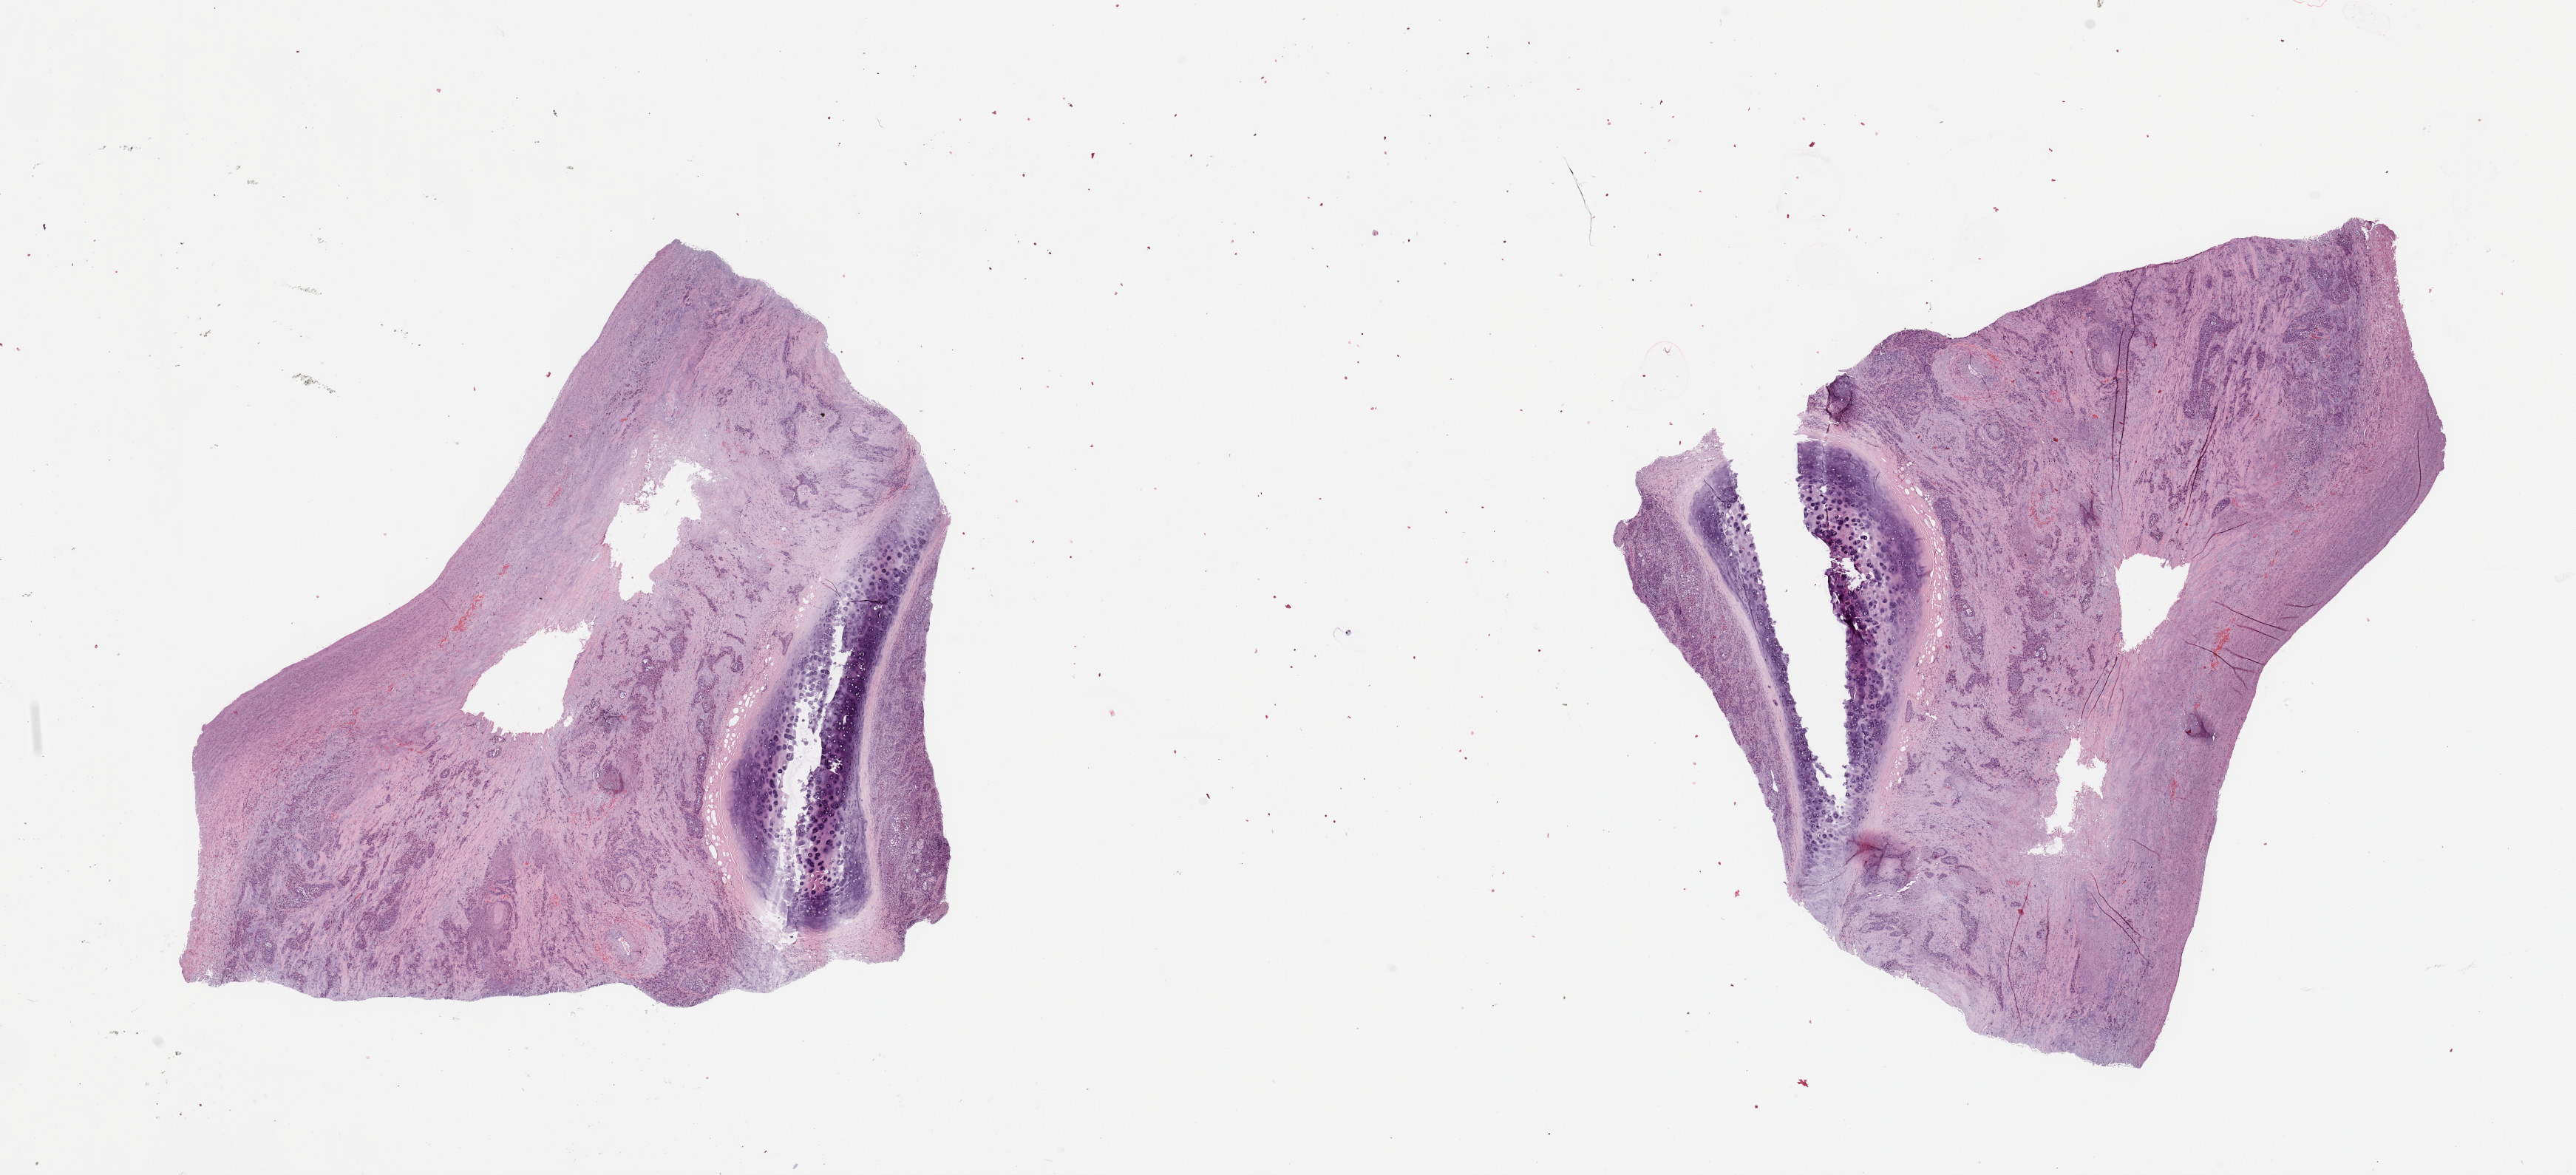
Hematoxylin and eosin (H&E) stained whole-slide image, whole scanned area (about 27.6 x 12.6 mm) shown as a low-resolution overview, tumour tissue sample, lung. 72-year-old male patient. Histologic grade: G3 (poorly differentiated).
Histologic diagnosis: Squamous cell carcinoma, NOS. AJCC pathologic stage: IIA.